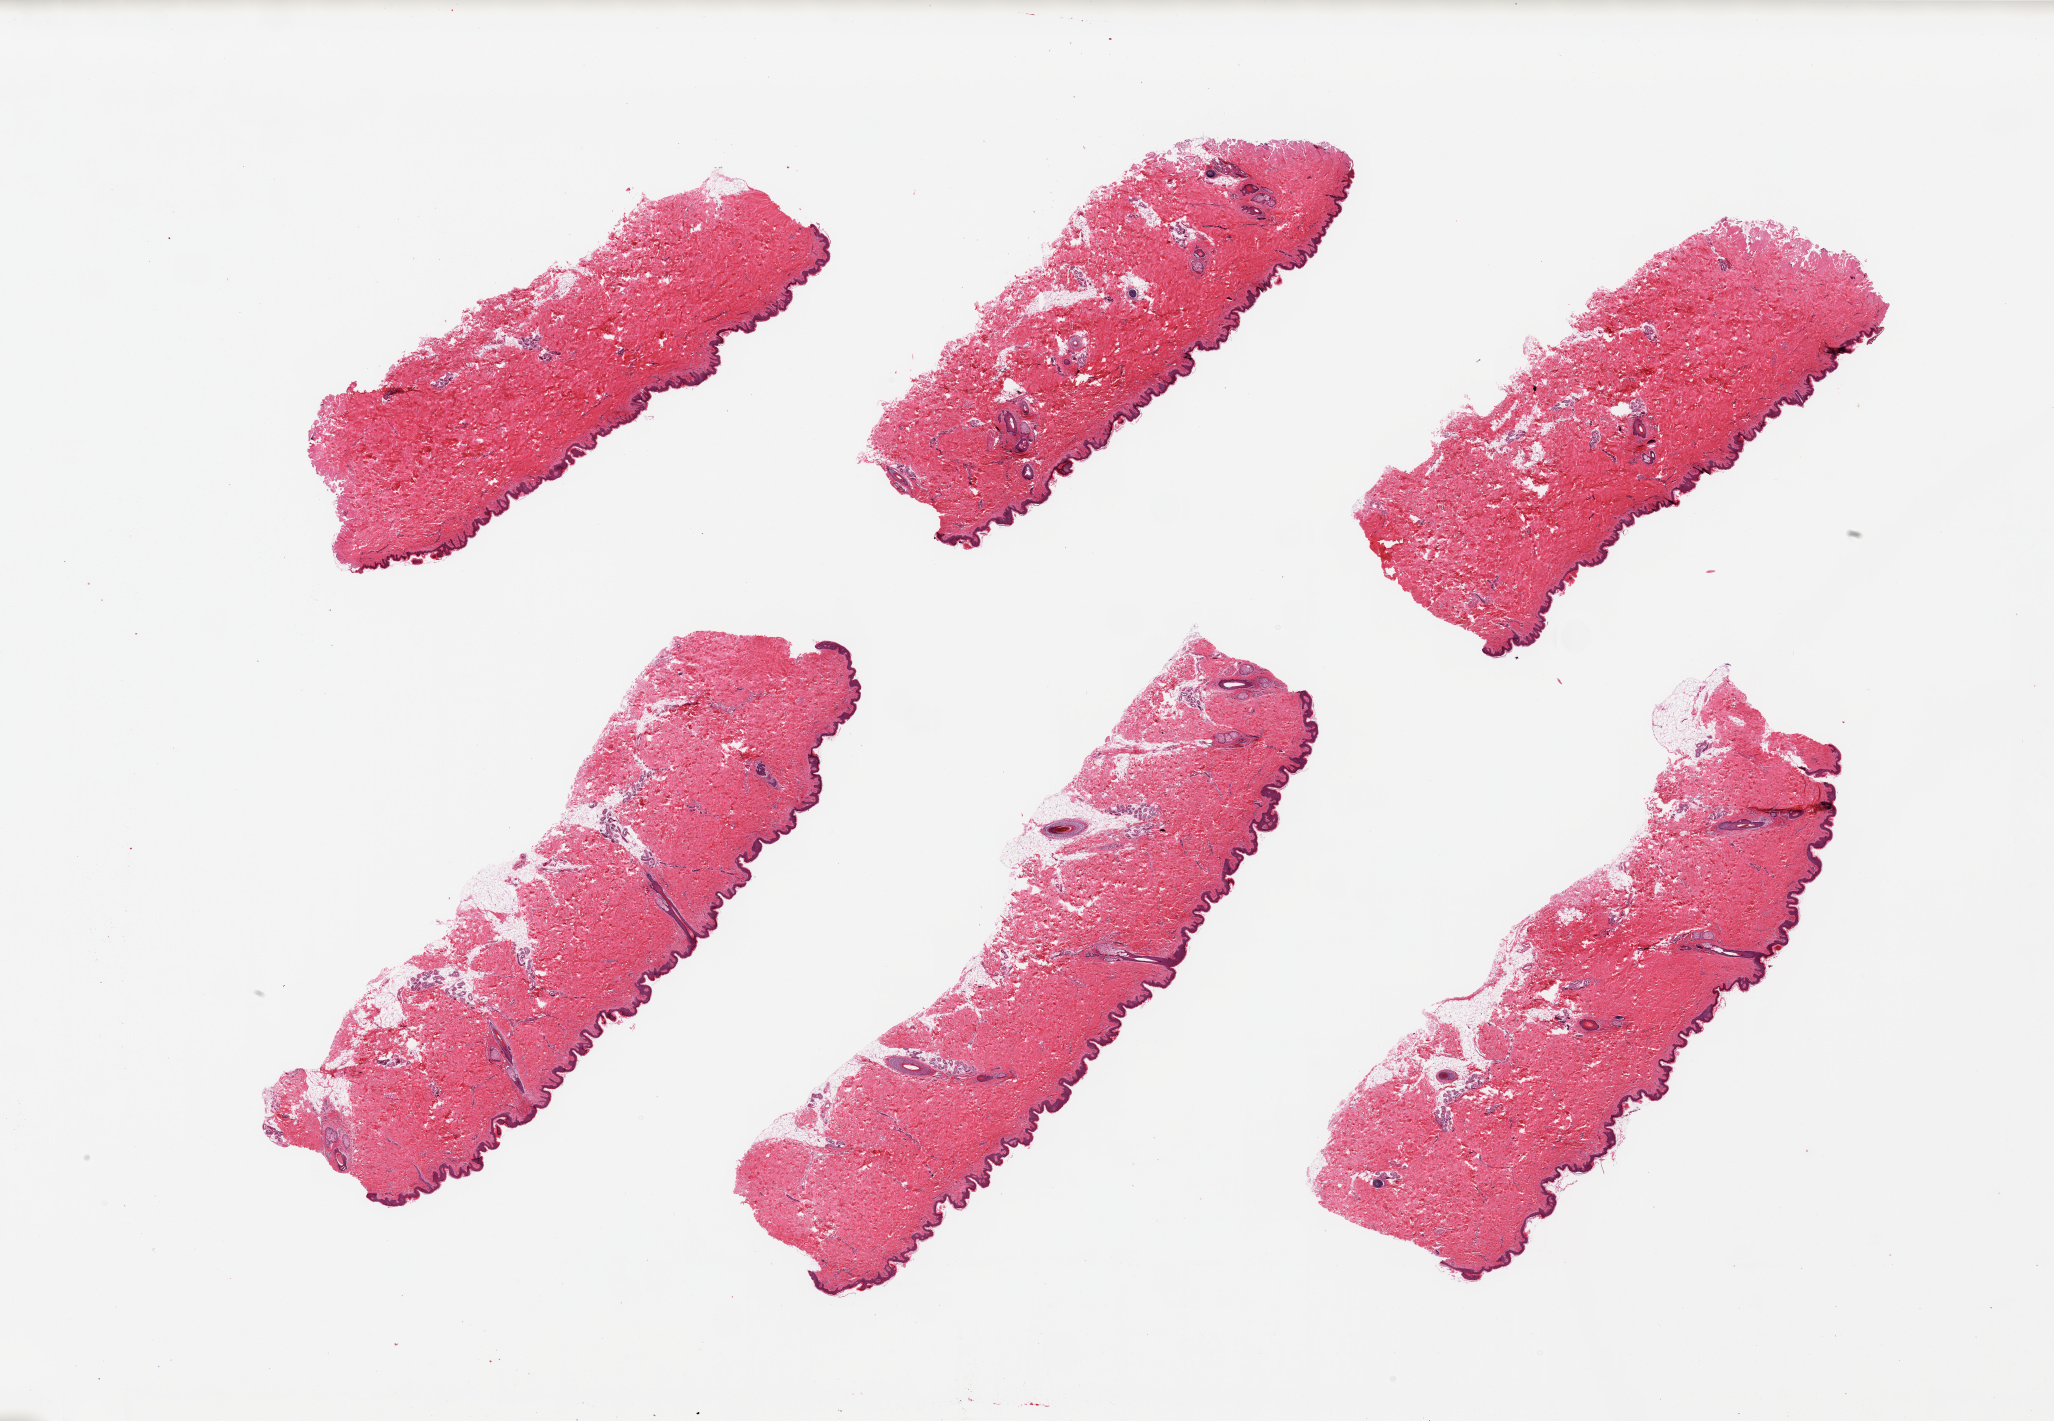
Haematoxylin and eosin whole-slide image, a low-resolution overview of the entire scanned area, about 32.5 x 22.5 mm. PAXgene-fixed paraffin-embedded (PFPE) section. Target tissue: skin of suprapubic region. Tissue donor sample.
Pathologist's review note for this sample: 6 pieces; includes up to ~5-10% attached/internal fat, hair bearing sklin.